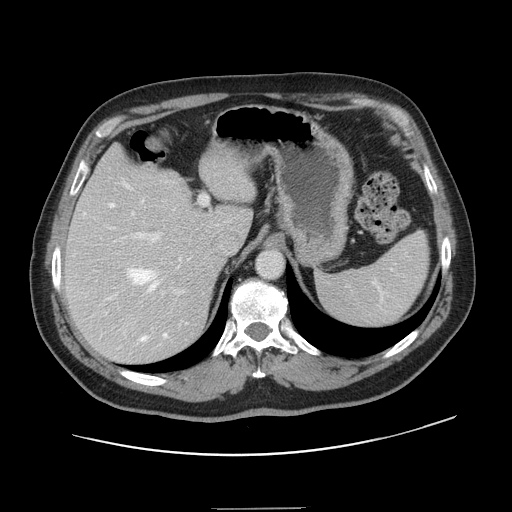
Contrast-enhanced abdominal CT, one axial slice; slice 100 of 143 in the series (ordered by position); intravenous contrast given; soft-tissue window (W 400 / L 40 HU); 2.5 mm slice thickness; 512 × 512 image matrix, field of view 402 × 402 mm. Male patient, age 62 years. From the clinical record (not read from this slice): diagnosis: colorectal cancer liver metastases, imaged before liver resection; multiple liver metastases: yes; largest metastasis: 2.7 cm; disease in both lobes: no.
Annotated regions visible in this slice (manually delineated by an expert):
- hepatic veins: box from (x=84, y=184) to (x=181, y=341) px
- liver: (x=66, y=148)–(x=255, y=363)
- planned liver remnant (the part of the liver to remain after resection): (x=66, y=148)–(x=254, y=263)
- portal vein (with intrahepatic branches): (x=111, y=195)–(x=208, y=294)